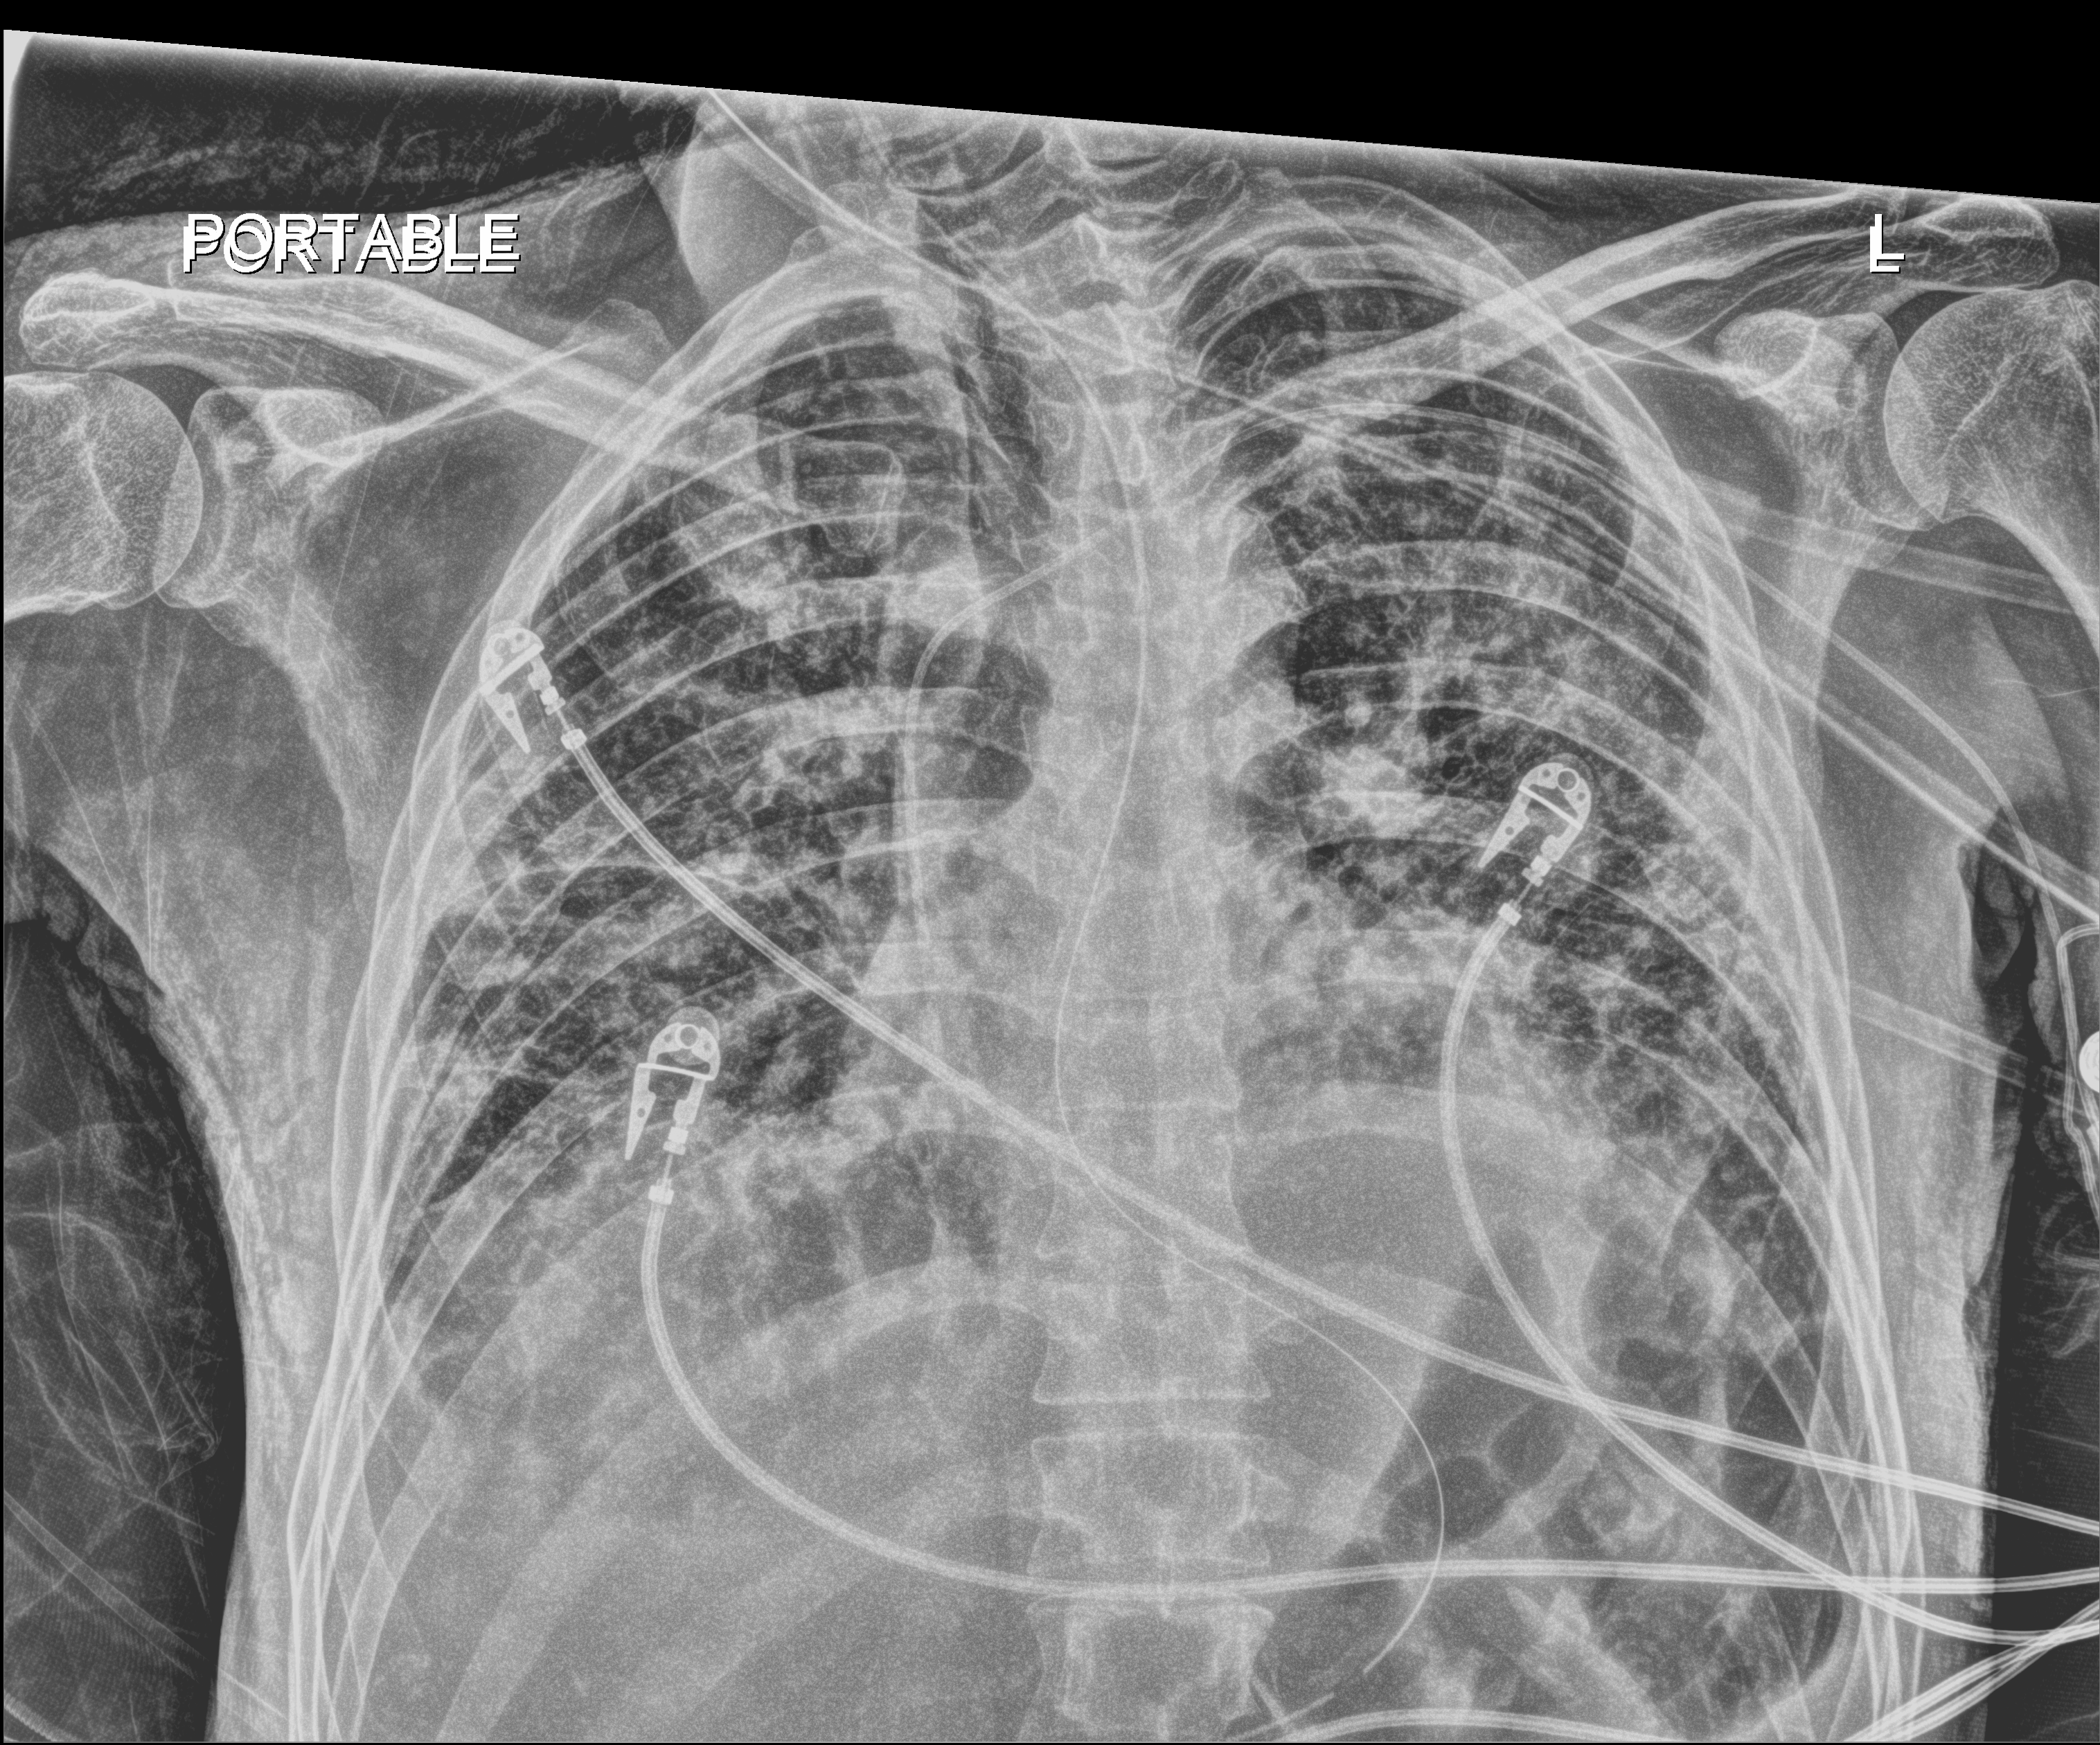
Bedside chest radiograph (digital radiography); anteroposterior (AP) projection. Patient hospitalised with COVID-19; male, aged 18–59 years.
Admission-level facts for this patient (not findings on this image; timing relative to this image not recorded): admitted to intensive care during this hospital stay: yes; mechanically ventilated during this hospital stay: yes; other chronic lung disease (admission record): no.